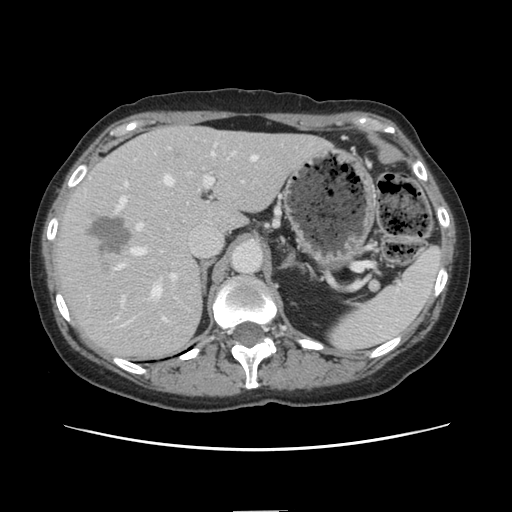
Contrast-enhanced abdominal CT, one axial slice. Position 94 of 141 along the scan axis. Intravenous contrast given. Soft-tissue window (W 400 / L 40 HU). 2.5 mm slice thickness. 512 × 512 image matrix, field of view 350 × 350 mm. Female patient, age 63 years. From the clinical record (not read from this slice): diagnosis: colorectal cancer liver metastases, imaged before liver resection; multiple liver metastases: yes; largest metastasis: 3.2 cm; disease in both lobes: yes.
Outlined on this slice (manually delineated by an expert):
- hepatic veins: bounding box [x1, y1, x2, y2] px = [119, 153, 257, 322]
- liver: [55, 127, 328, 360]
- planned liver remnant (the part of the liver to remain after resection): [182, 127, 328, 234]
- portal vein (with intrahepatic branches): [116, 149, 239, 300]